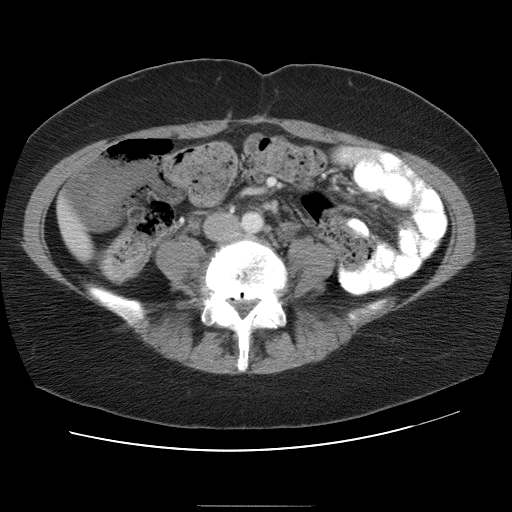
Contrast-enhanced abdominal CT, one axial slice; position 3 of 30 along the scan axis; reconstruction kernel STANDARD; 120 kVp; intravenous contrast given; soft-tissue window (W 400 / L 40 HU); 7.5 mm slice thickness; 512 × 512 image matrix, field of view 376 × 376 mm. Female patient, age 52 years. From the clinical record (not read from this slice): diagnosis: colorectal cancer liver metastases, imaged before liver resection; multiple liver metastases: no; largest metastasis: 3 cm; disease in both lobes: yes.
Outlined on this slice (manually delineated by an expert):
- liver: bounding box <59,203,91,257> (left, top, right, bottom; pixels)